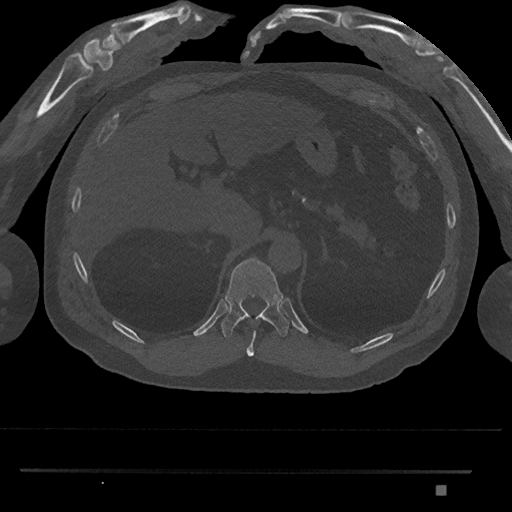
CT including the spine, one axial slice; position 958 of 1134 along the scan axis; reconstruction kernel Br40s/3; bone window (W 1800 / L 400 HU); 0.5 mm slice thickness; 512 × 512 image matrix, field of view 429 × 429 mm. Patient: male, 65 years. From the clinical record (not read from this slice): primary cancer: prostate.
Annotated regions visible in this slice (semi-automatically segmented with operator editing):
- T10 vertebra: bounding box <246,331,256,357> (left, top, right, bottom; pixels)
- T11 vertebra: <221,258,289,338>